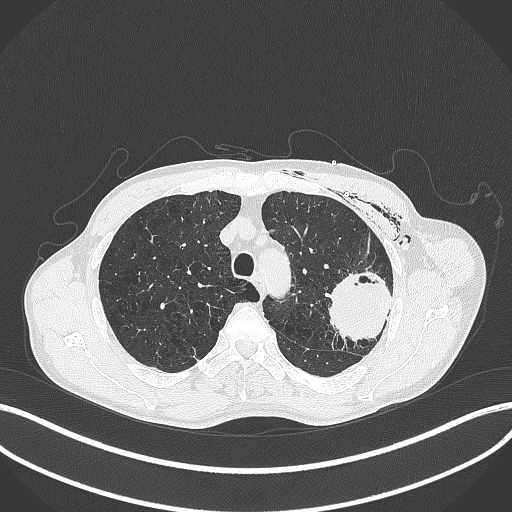
Chest CT, one axial slice. Slice 312 of 457 in the series (ordered by position). Reconstruction kernel B70f. 120 kVp. Lung window (W 1500 / L -600 HU). 1 mm slice thickness. 512 × 512 image matrix, field of view 400 × 400 mm. Male patient, age 58 years. Case-level facts recorded for this patient, not image findings: clinical TNM (as recorded): T3 N0 M0.
Annotated regions visible in this slice (rectangle marked by the reading radiologist):
- lung tumour (recorded histology: adenocarcinoma): bounding box <324,271,397,343> (left, top, right, bottom; pixels)